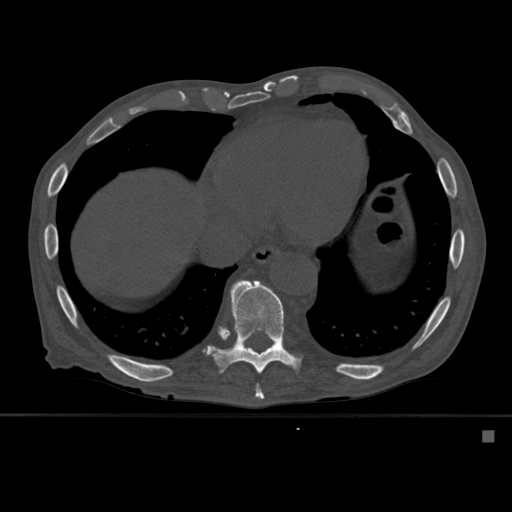
CT including the spine, one axial slice. Slice 316 of 527 in the series (ordered by position). Bone window (W 1800 / L 400 HU). 1.5 mm slice thickness. 512 × 512 image matrix, field of view 373 × 373 mm. Patient: male, 78 years. From the clinical record (not read from this slice): primary cancer: prostate.
Structures marked on this image (semi-automatic segmentation, software-assisted and operator-edited):
- T10 vertebra: bounding box [x1, y1, x2, y2] px = [207, 280, 302, 374]
- T9 vertebra: [255, 384, 264, 400]